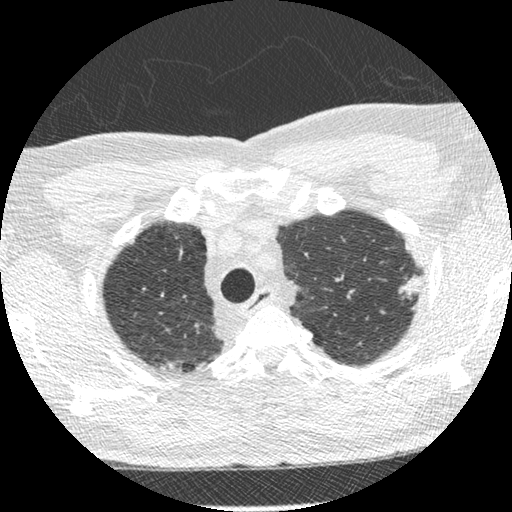
Low-dose screening chest CT, one axial slice. Slice 238 of 275 in the series (ordered by position). 120 kVp. Lung window (W 1500 / L -600 HU). 1.25 mm slice thickness. 512 × 512 image matrix, field of view 330 × 330 mm.
Outlined on this slice (expert manual segmentation):
- lesion 1 (tumor, upper lobe of left lung): bounding box [x1, y1, x2, y2] px = [399, 275, 420, 299]